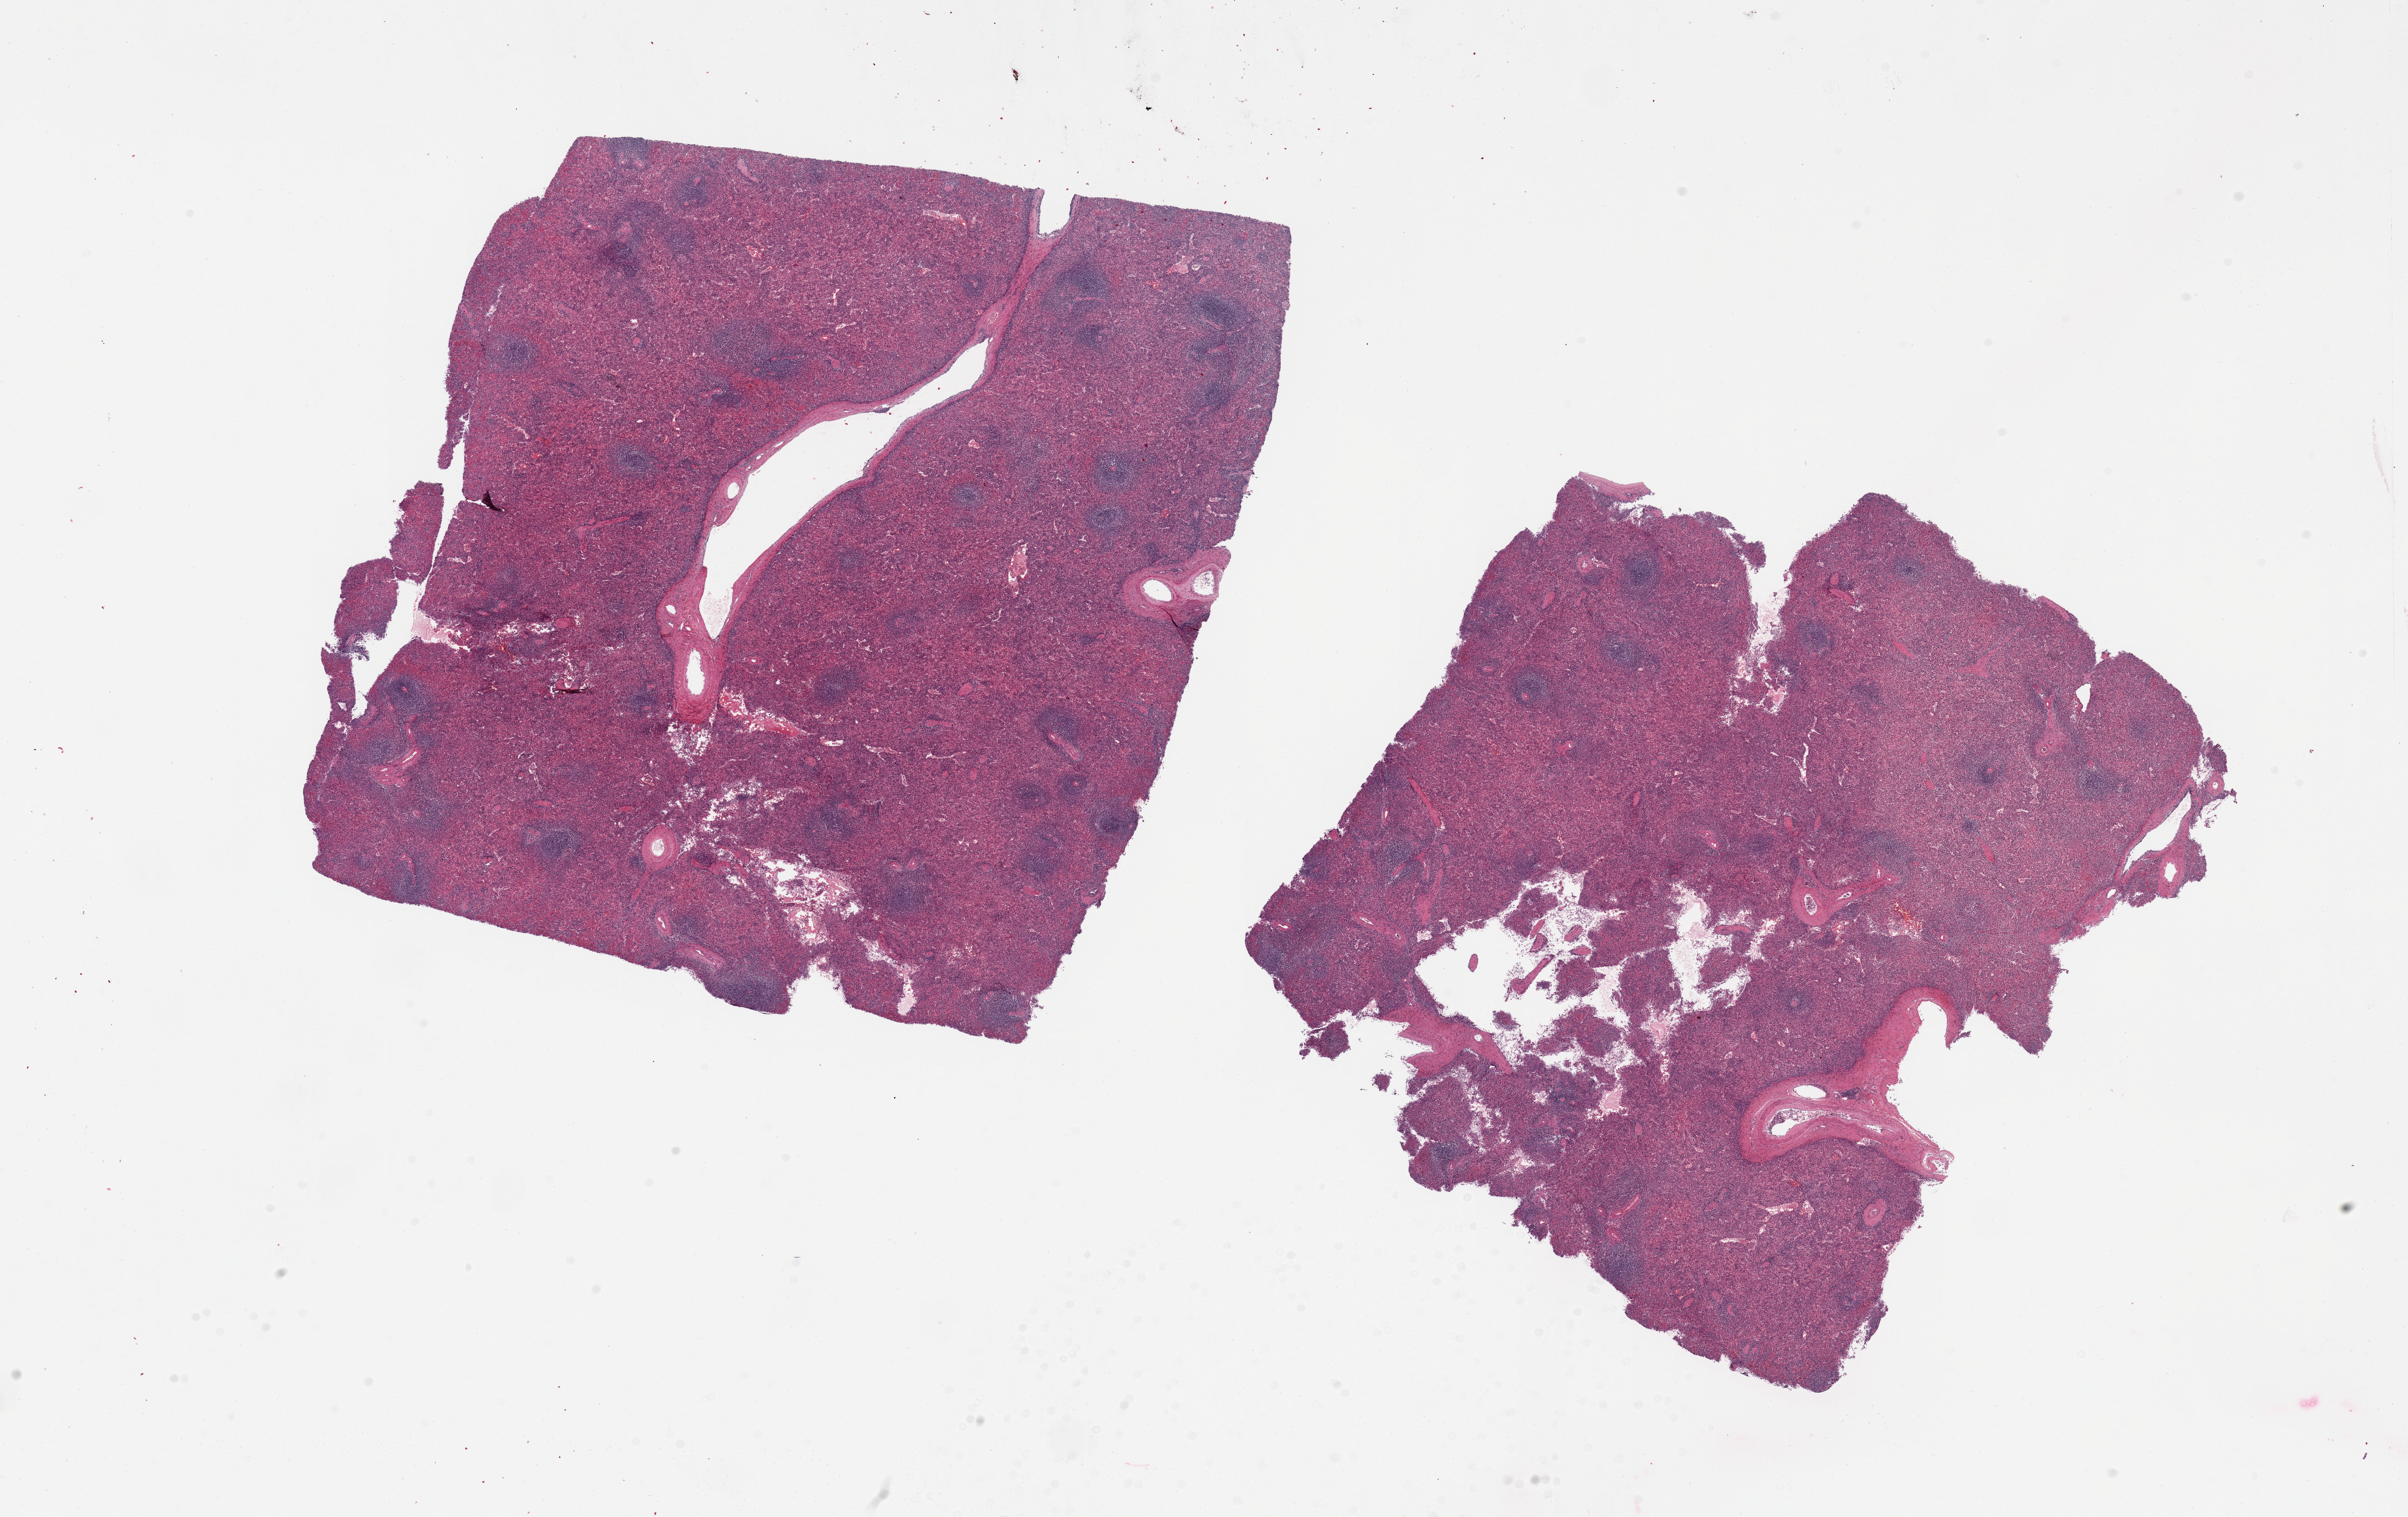
Hematoxylin and eosin (H&E) whole-slide image, brightfield — a low-resolution overview of the entire scanned area, about 30.5 x 19.2 mm; PAXgene-fixed paraffin-embedded (PFPE) section; section of spleen (target tissue); donor tissue sample. Female donor.
• pathologist's review note for this sample: 2 pieces, 11x11 & 11x10mm